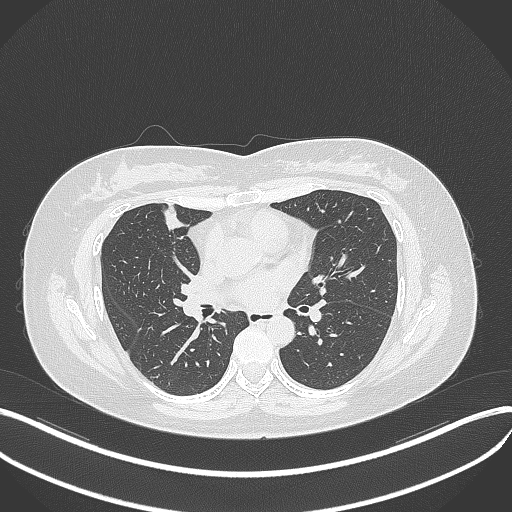
Chest CT, one axial slice; slice 164 of 273 in the series (ordered by position); 120 kVp; lung window (W 1500 / L -600 HU); 1 mm slice thickness; 512 × 512 image matrix, field of view 400 × 400 mm. Patient: female, 42 years. Case-level facts recorded for this patient, not image findings: clinical TNM (as recorded): T1b N0 M0.
Structures marked on this image (bounding box drawn by a radiologist):
- lung tumour (recorded histology: adenocarcinoma): bounding box (x1, y1, x2, y2) in pixels: (160, 197, 191, 235)